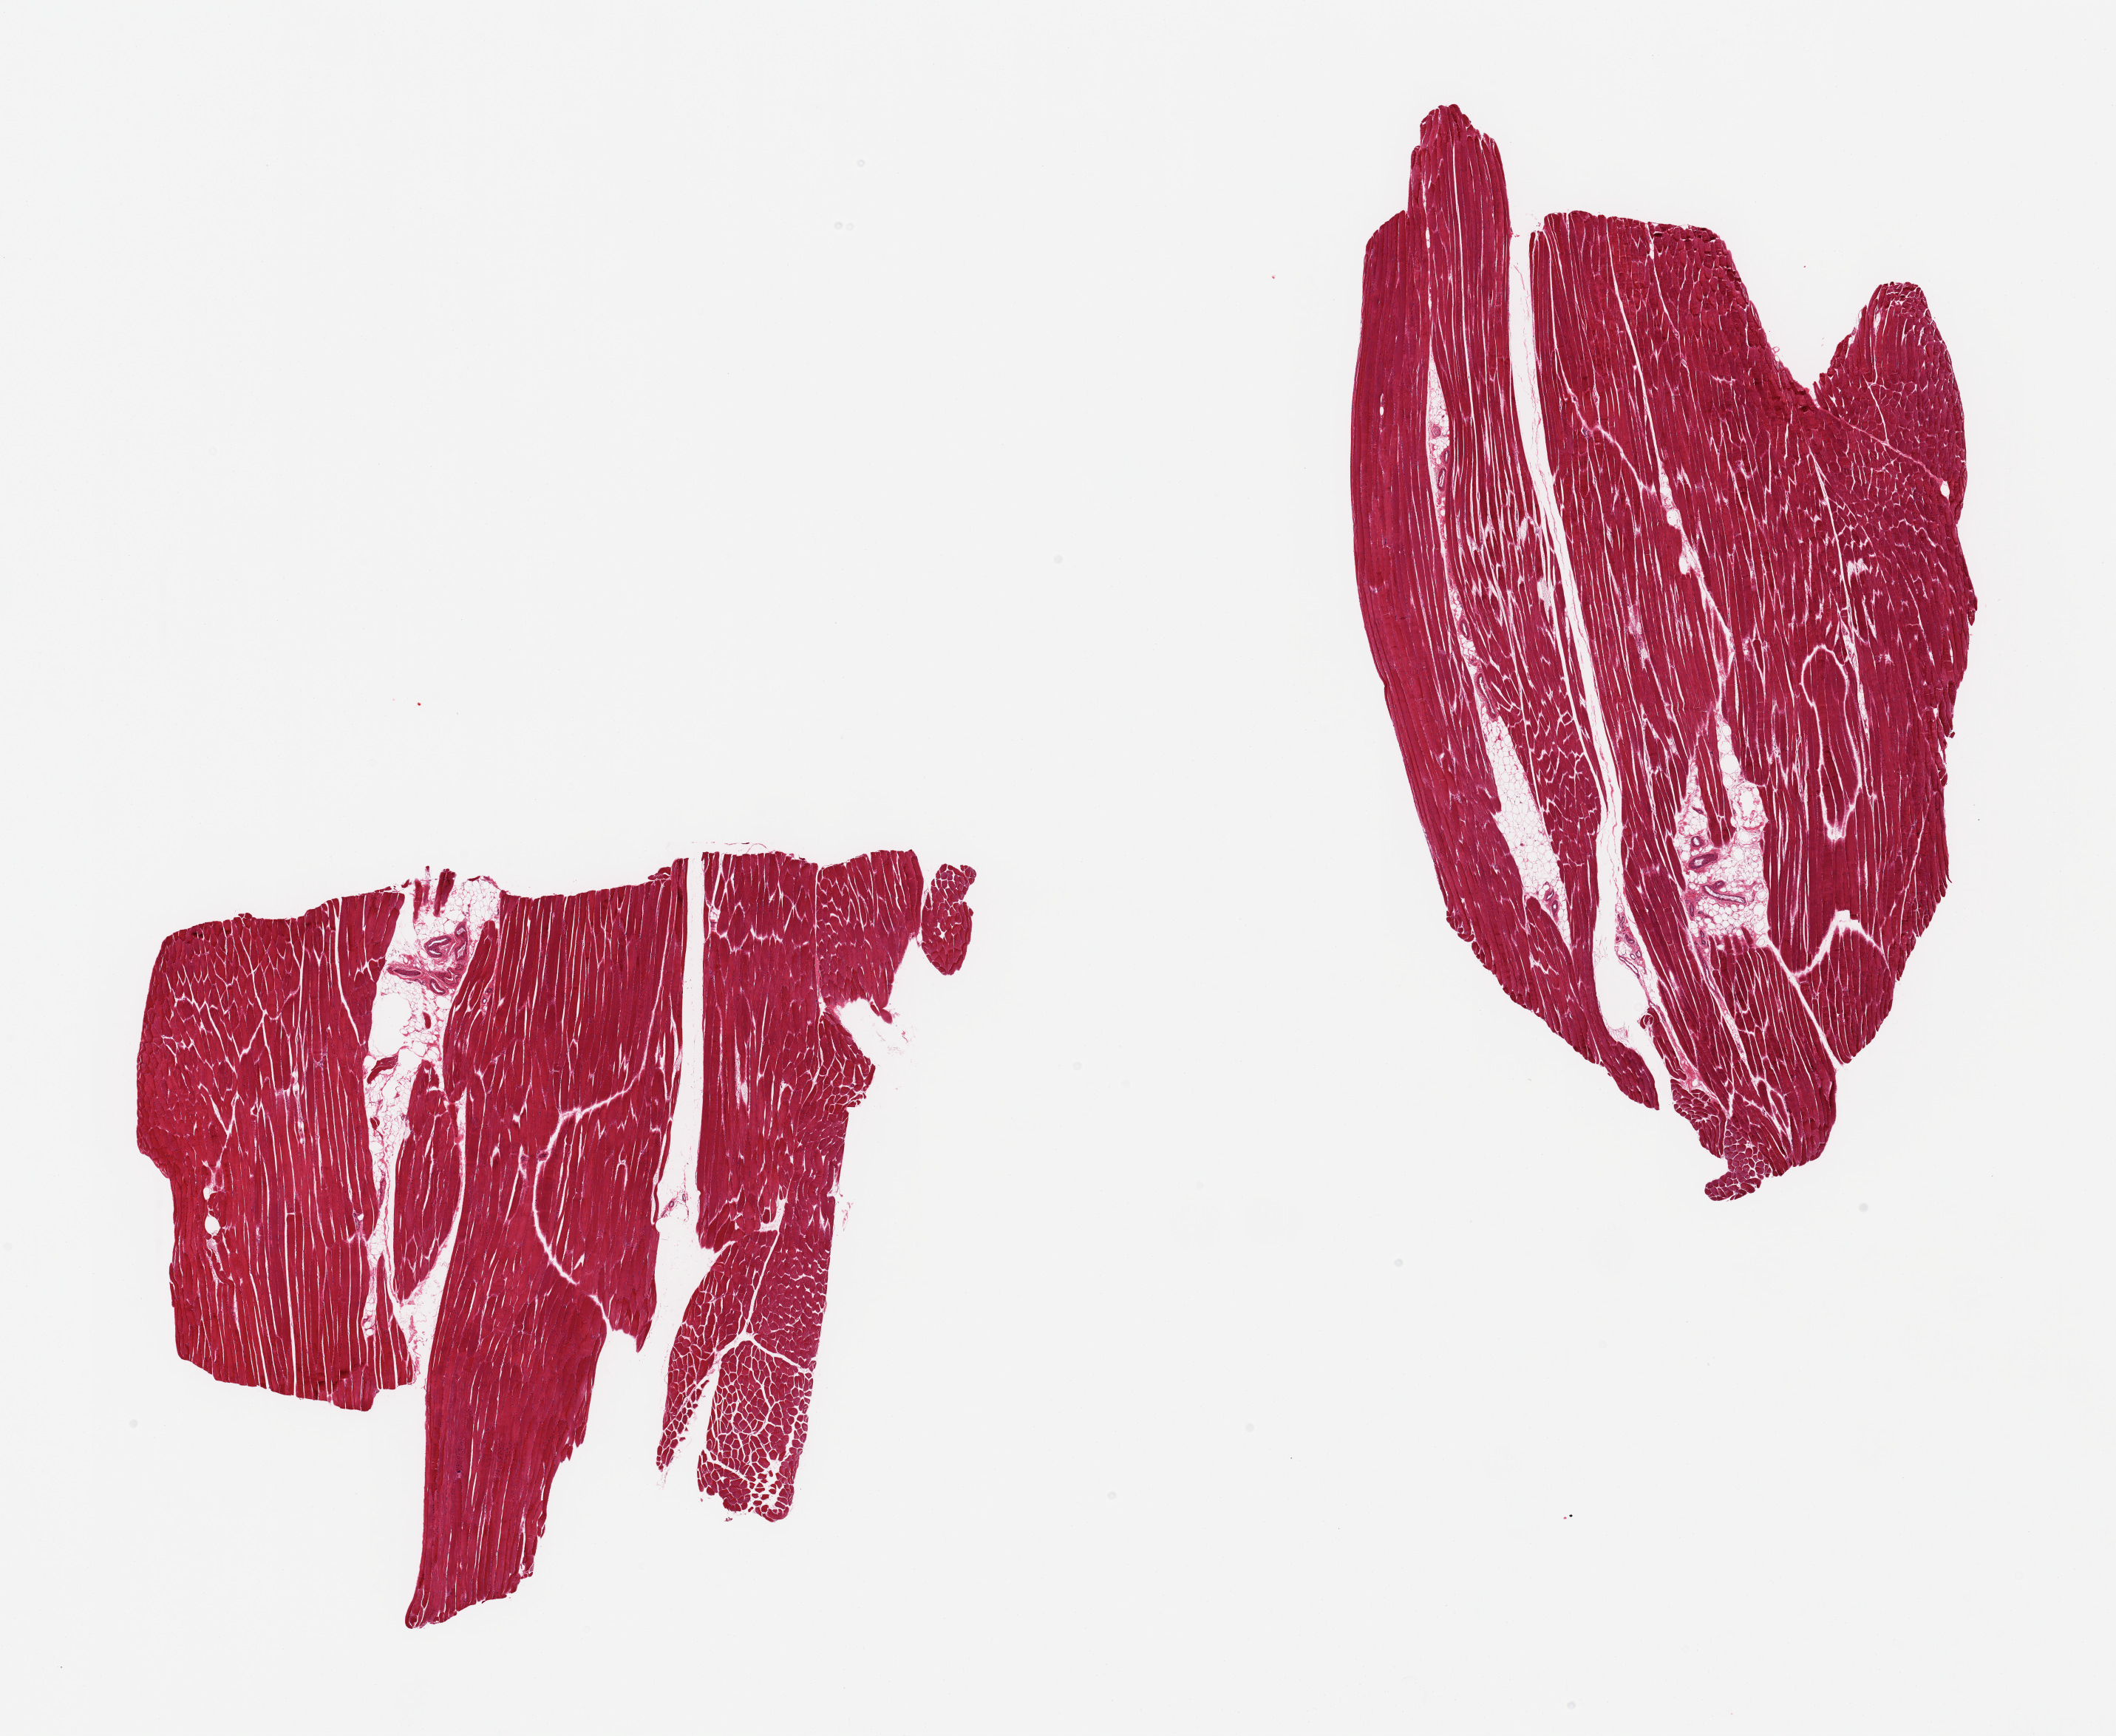
Digitized H&E-stained section — low-resolution overview of the scanned area, about 22.6 x 18.6 mm, PAXgene-fixed paraffin-embedded (PFPE) section, section of skeletal muscle (target tissue), donor tissue sample. Donor: male.
• review note (as recorded): 2 pieces; ~10% internal fat